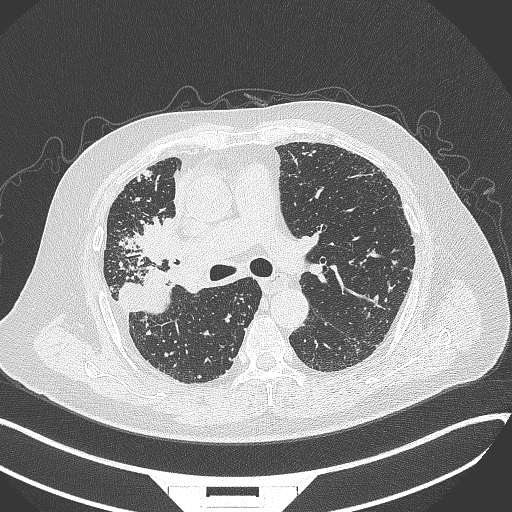
Chest CT, one axial slice; slice 212 of 384 in the series (ordered by position); reconstruction kernel B70f; 120 kVp; lung window (W 1500 / L -600 HU); 1 mm slice thickness; 512 × 512 image matrix, field of view 400 × 400 mm. Male patient, age 69 years. From the clinical record (not read from this slice): clinical TNM (as recorded): T4 N3 M1.
Structures marked on this image (rectangle marked by the reading radiologist):
- lung tumour (recorded histology: adenocarcinoma): bounding box [x1, y1, x2, y2] px = [133, 218, 181, 267]